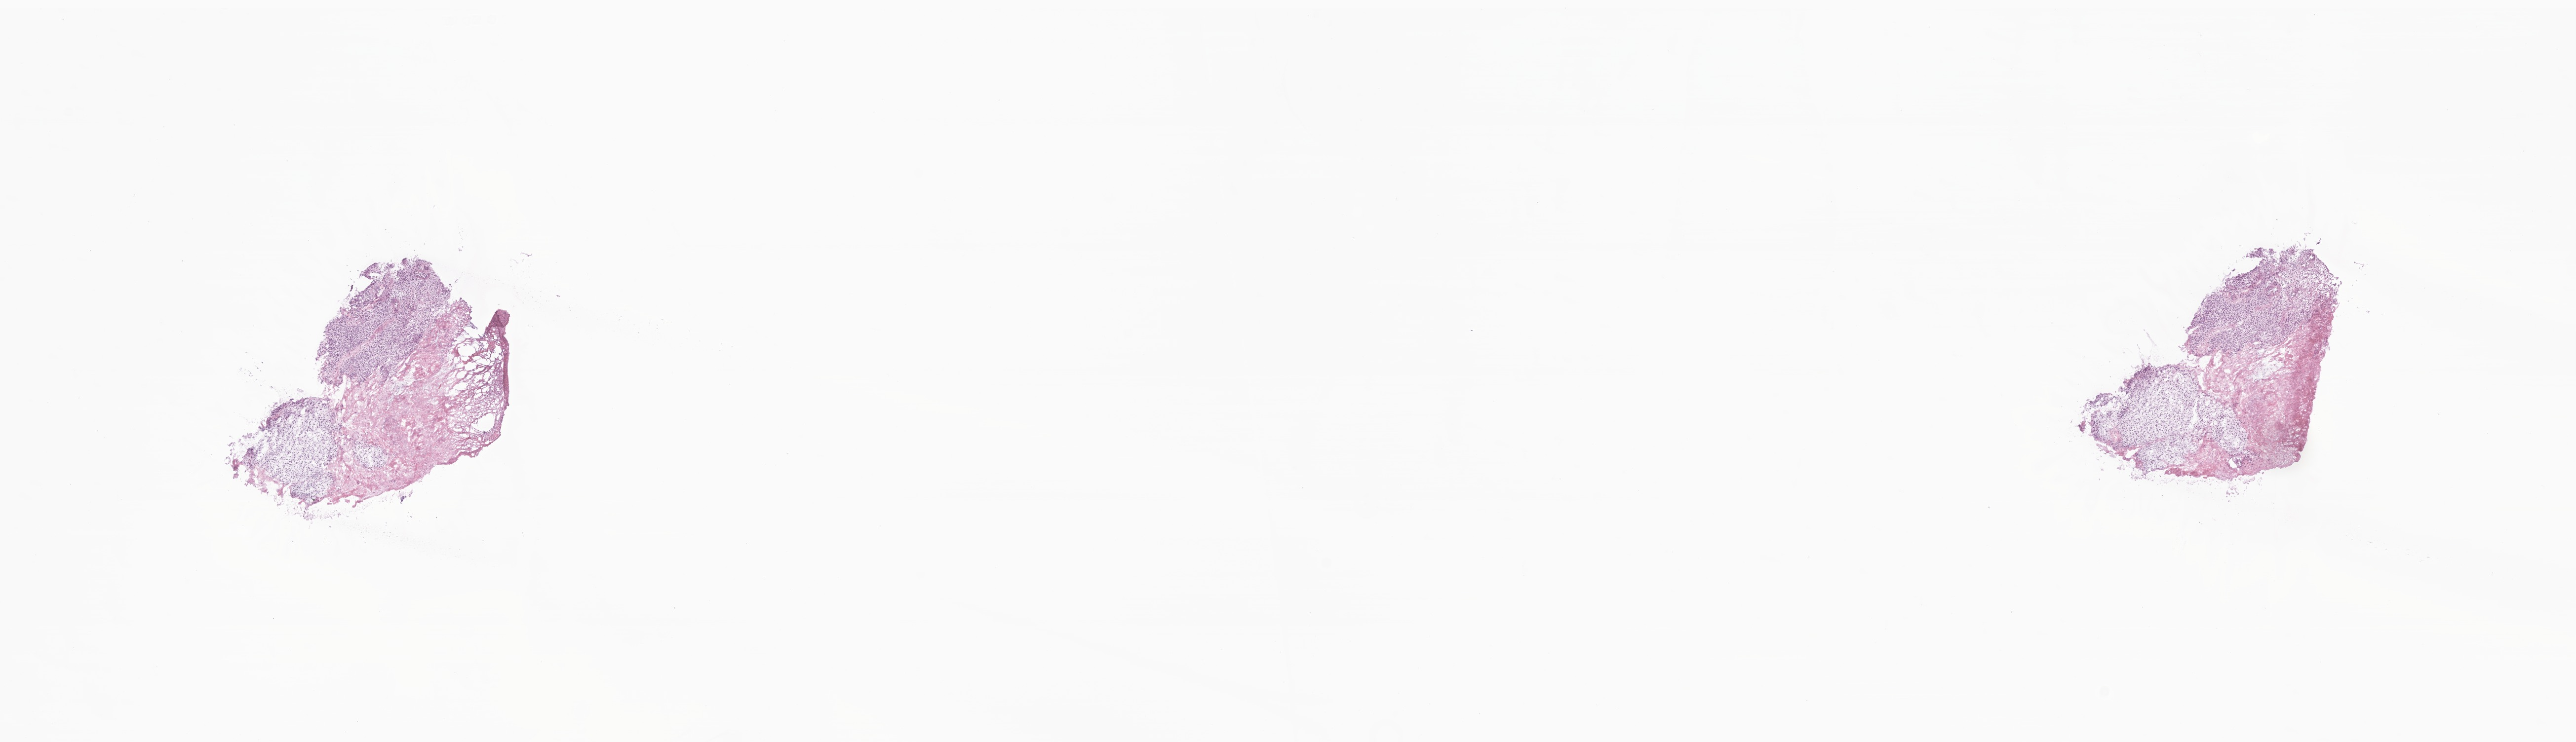
Hematoxylin and eosin (H&E) whole-slide image of tumor tissue from the anterior wall of nasopharynx — low-resolution overview of the scanned area, about 22.0 x 6.3 mm, cryosection (OCT / tissue freezing medium). Male patient, age 123 months (10 years 3 months).
Recorded diagnosis: Embryonal rhabdomyosarcoma, NOS.